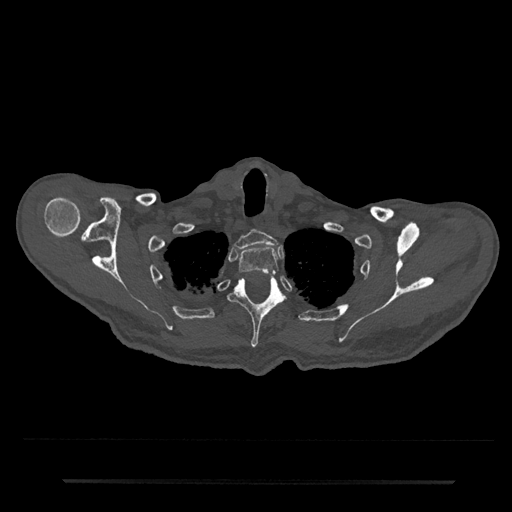
CT including the spine, one axial slice. Position 672 of 797 along the scan axis. Bone window (W 1800 / L 400 HU). 0.5 mm slice thickness. 512 × 512 image matrix, field of view 427 × 427 mm. Patient: male, 74 years. Case-level facts recorded for this patient, not image findings: primary cancer: prostate.
Outlined on this slice (semi-automatically segmented with operator editing):
- T1 vertebra: bounding box [x1, y1, x2, y2] px = [234, 230, 278, 249]
- T2 vertebra: [238, 246, 279, 276]
- T3 vertebra: [229, 275, 283, 348]